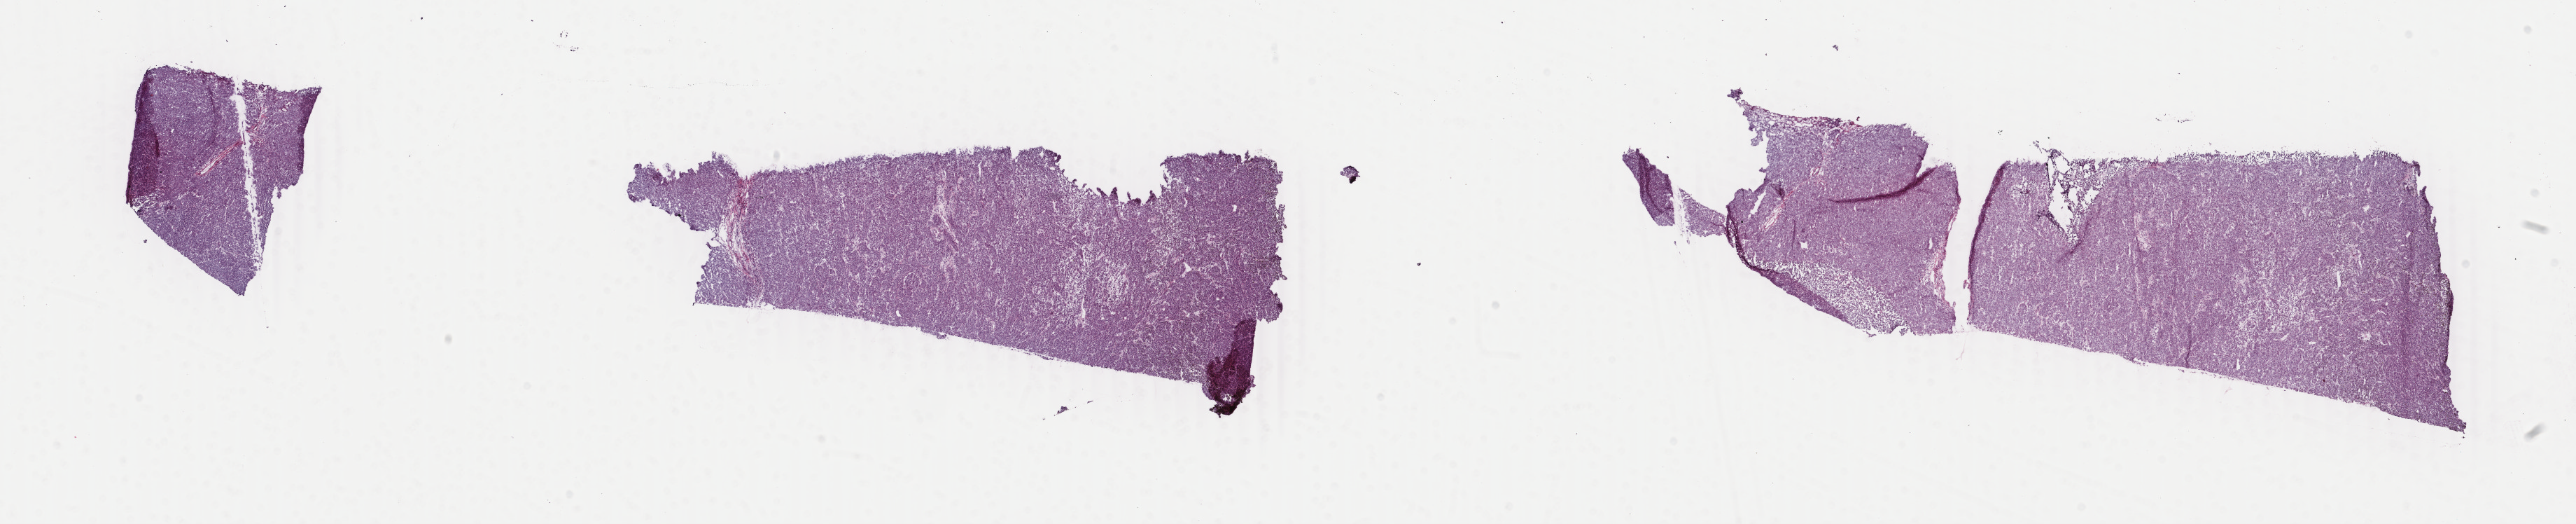
Digitized Hematoxylin and eosin (H&E) stained tissue section (whole slide) — shown as a low-resolution overview of the whole scanned area (about 29.3 x 5.9 mm, acquisition: 40x scan); frozen section; metastatic tumour sample, sampled site: lymph nodes of inguinal region or leg. Male, age 55 years at initial diagnosis. Slide review estimates, as recorded: tumour cells 100%, tumour nuclei 85%, normal cells 0%, stromal cells 0%, necrosis 0%. Inflammatory infiltration, as recorded: lymphocyte infiltration 1%, monocyte infiltration 0%, neutrophil infiltration 0%.
* this section: metastatic tumour tissue
* patient diagnosis: Malignant melanoma, NOS